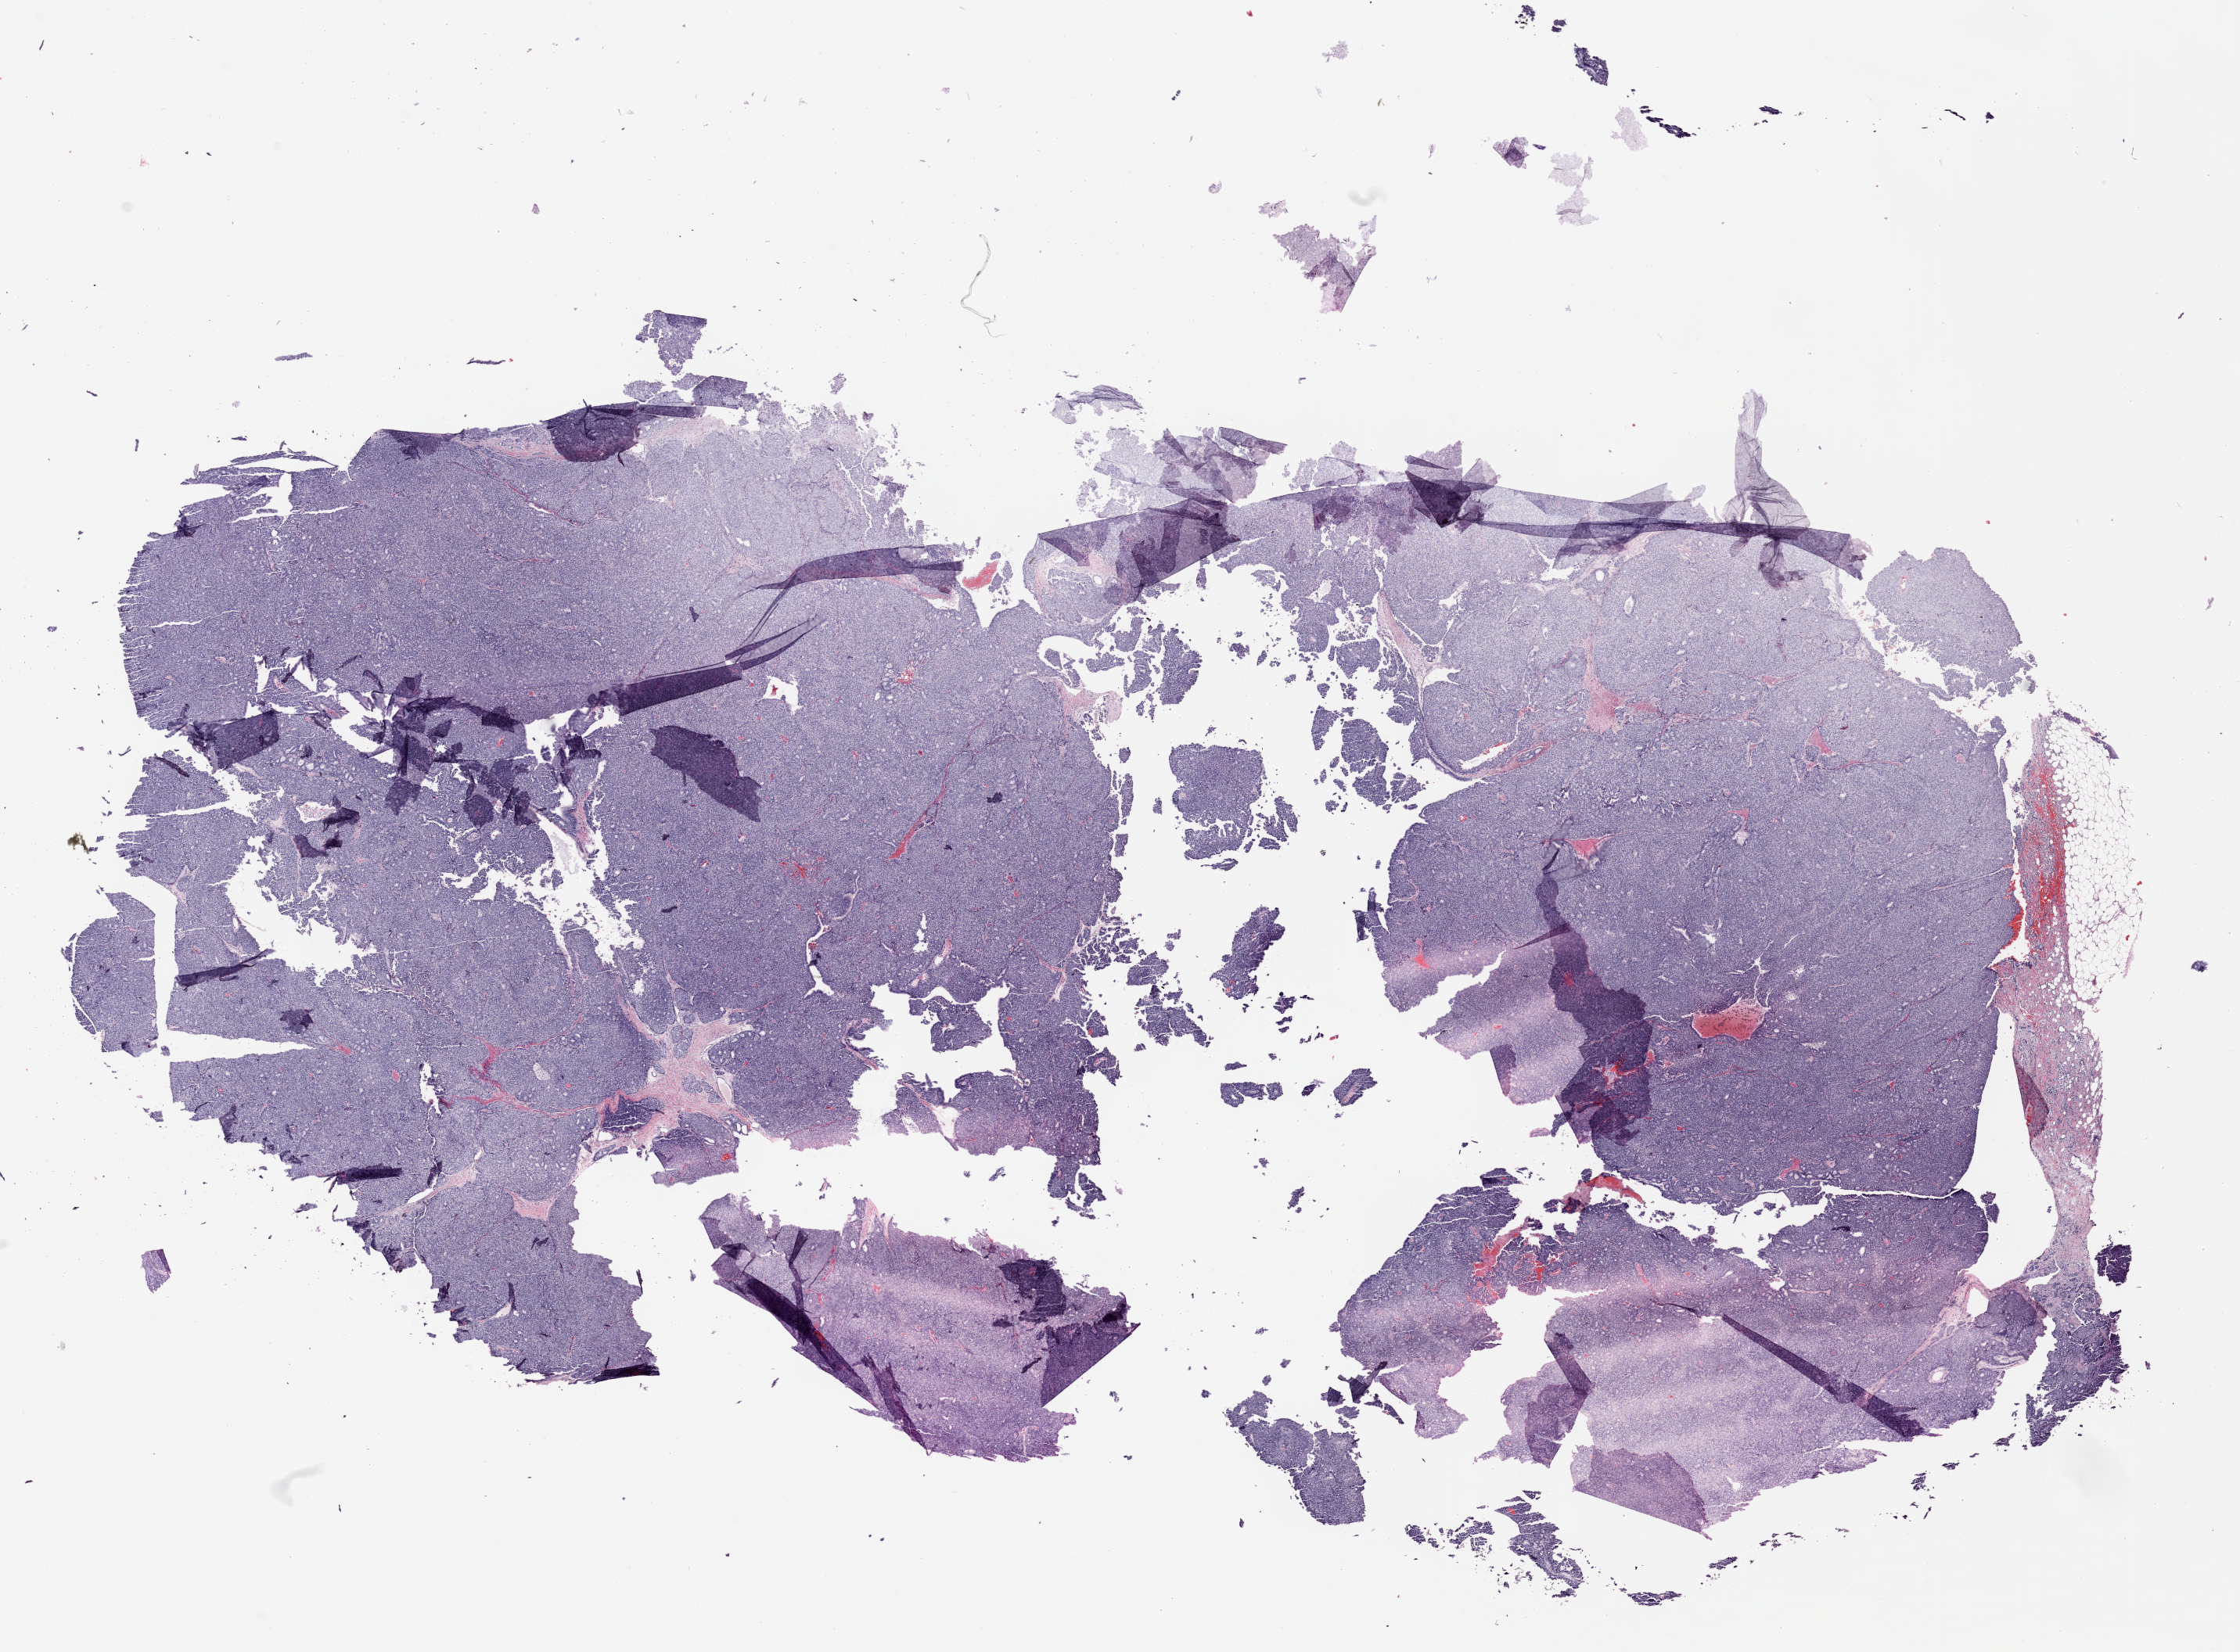
Whole-slide histology image, H&E-stained, low-resolution overview of the scanned area, about 22.9 x 16.9 mm. Formalin-fixed paraffin-embedded (FFPE) diagnostic section. Sample: primary tumour, breast. Female, age 72 years at initial diagnosis.
Pathologic diagnosis: Papillary carcinoma, NOS.